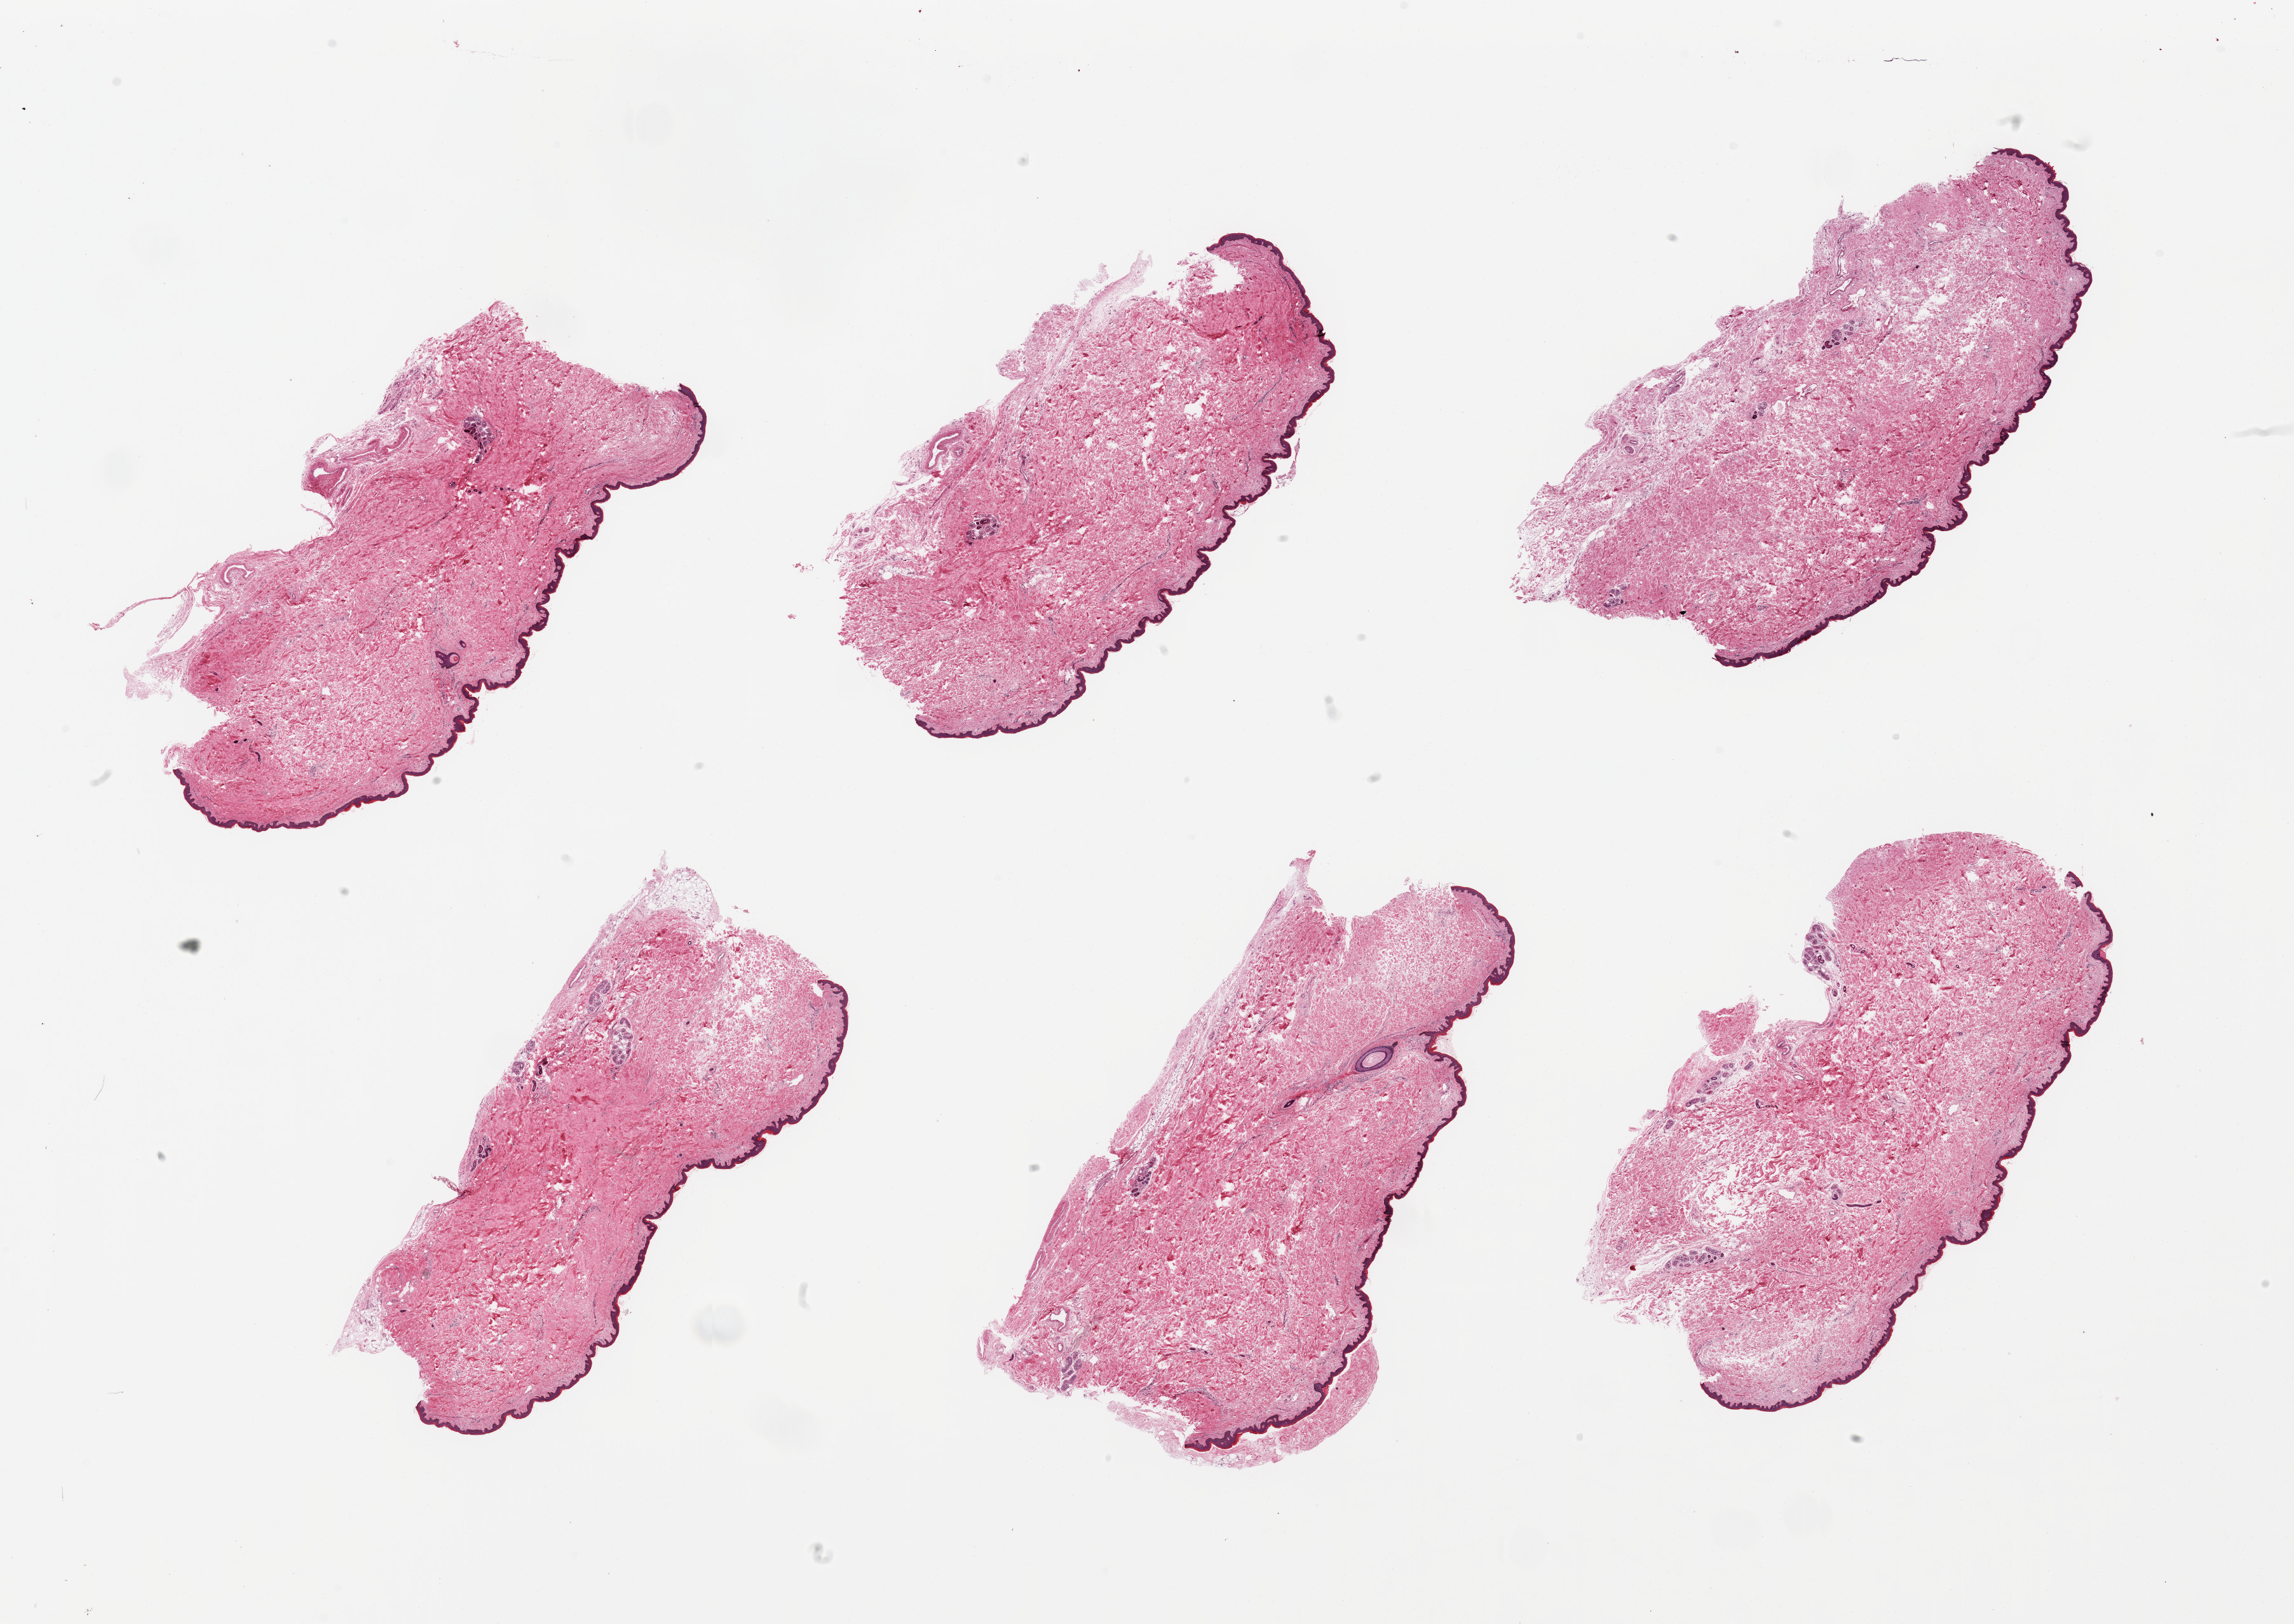
H&E whole-slide image — a low-resolution overview of the entire scanned area, about 28.5 x 20.2 mm (from a 20x scan). PAXgene-fixed, paraffin-embedded tissue. Sampled site (target tissue): skin of suprapubic region. Donor tissue sample.
* reviewer comment on this tissue sample: 6 pieces, minimal dermal fat; squamous epithelium is ~50-60 microns